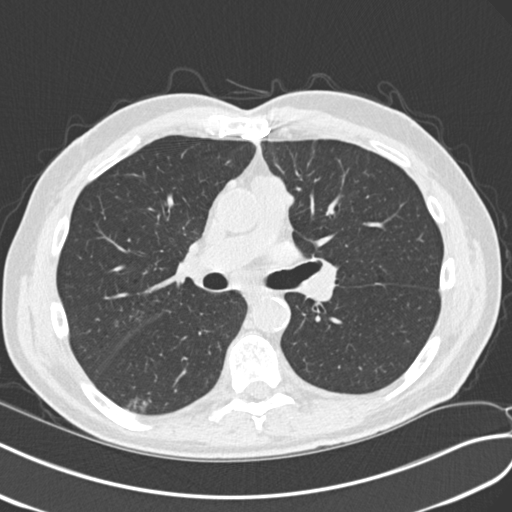
Low-dose screening chest CT, axial slice. Second annual screen. Lung window (W 1500 / L -600 HU). 2 mm slice thickness. Standard (soft-tissue) reconstruction kernel (B30f). 120 kVp. 512 × 512 image matrix, field of view 354 × 354 mm. Male participant, aged 68 years at enrolment. Current smoker at enrolment.
• Expert reader's lesion annotation, bounding box <114,387,163,423> (left, top, right, bottom; pixels).
• The screening reader recorded 4 non-calcified nodules or masses ≥4 mm on this exam (right upper lobe, left upper lobe, right upper lobe, right lower lobe); which of them this box marks is not recorded.
• Lung cancer was diagnosed 653 days after this screen: non-small cell carcinoma, right lower lobe, poorly differentiated (G3), stage IA (AJCC 6th edition), 23 mm at pathology.